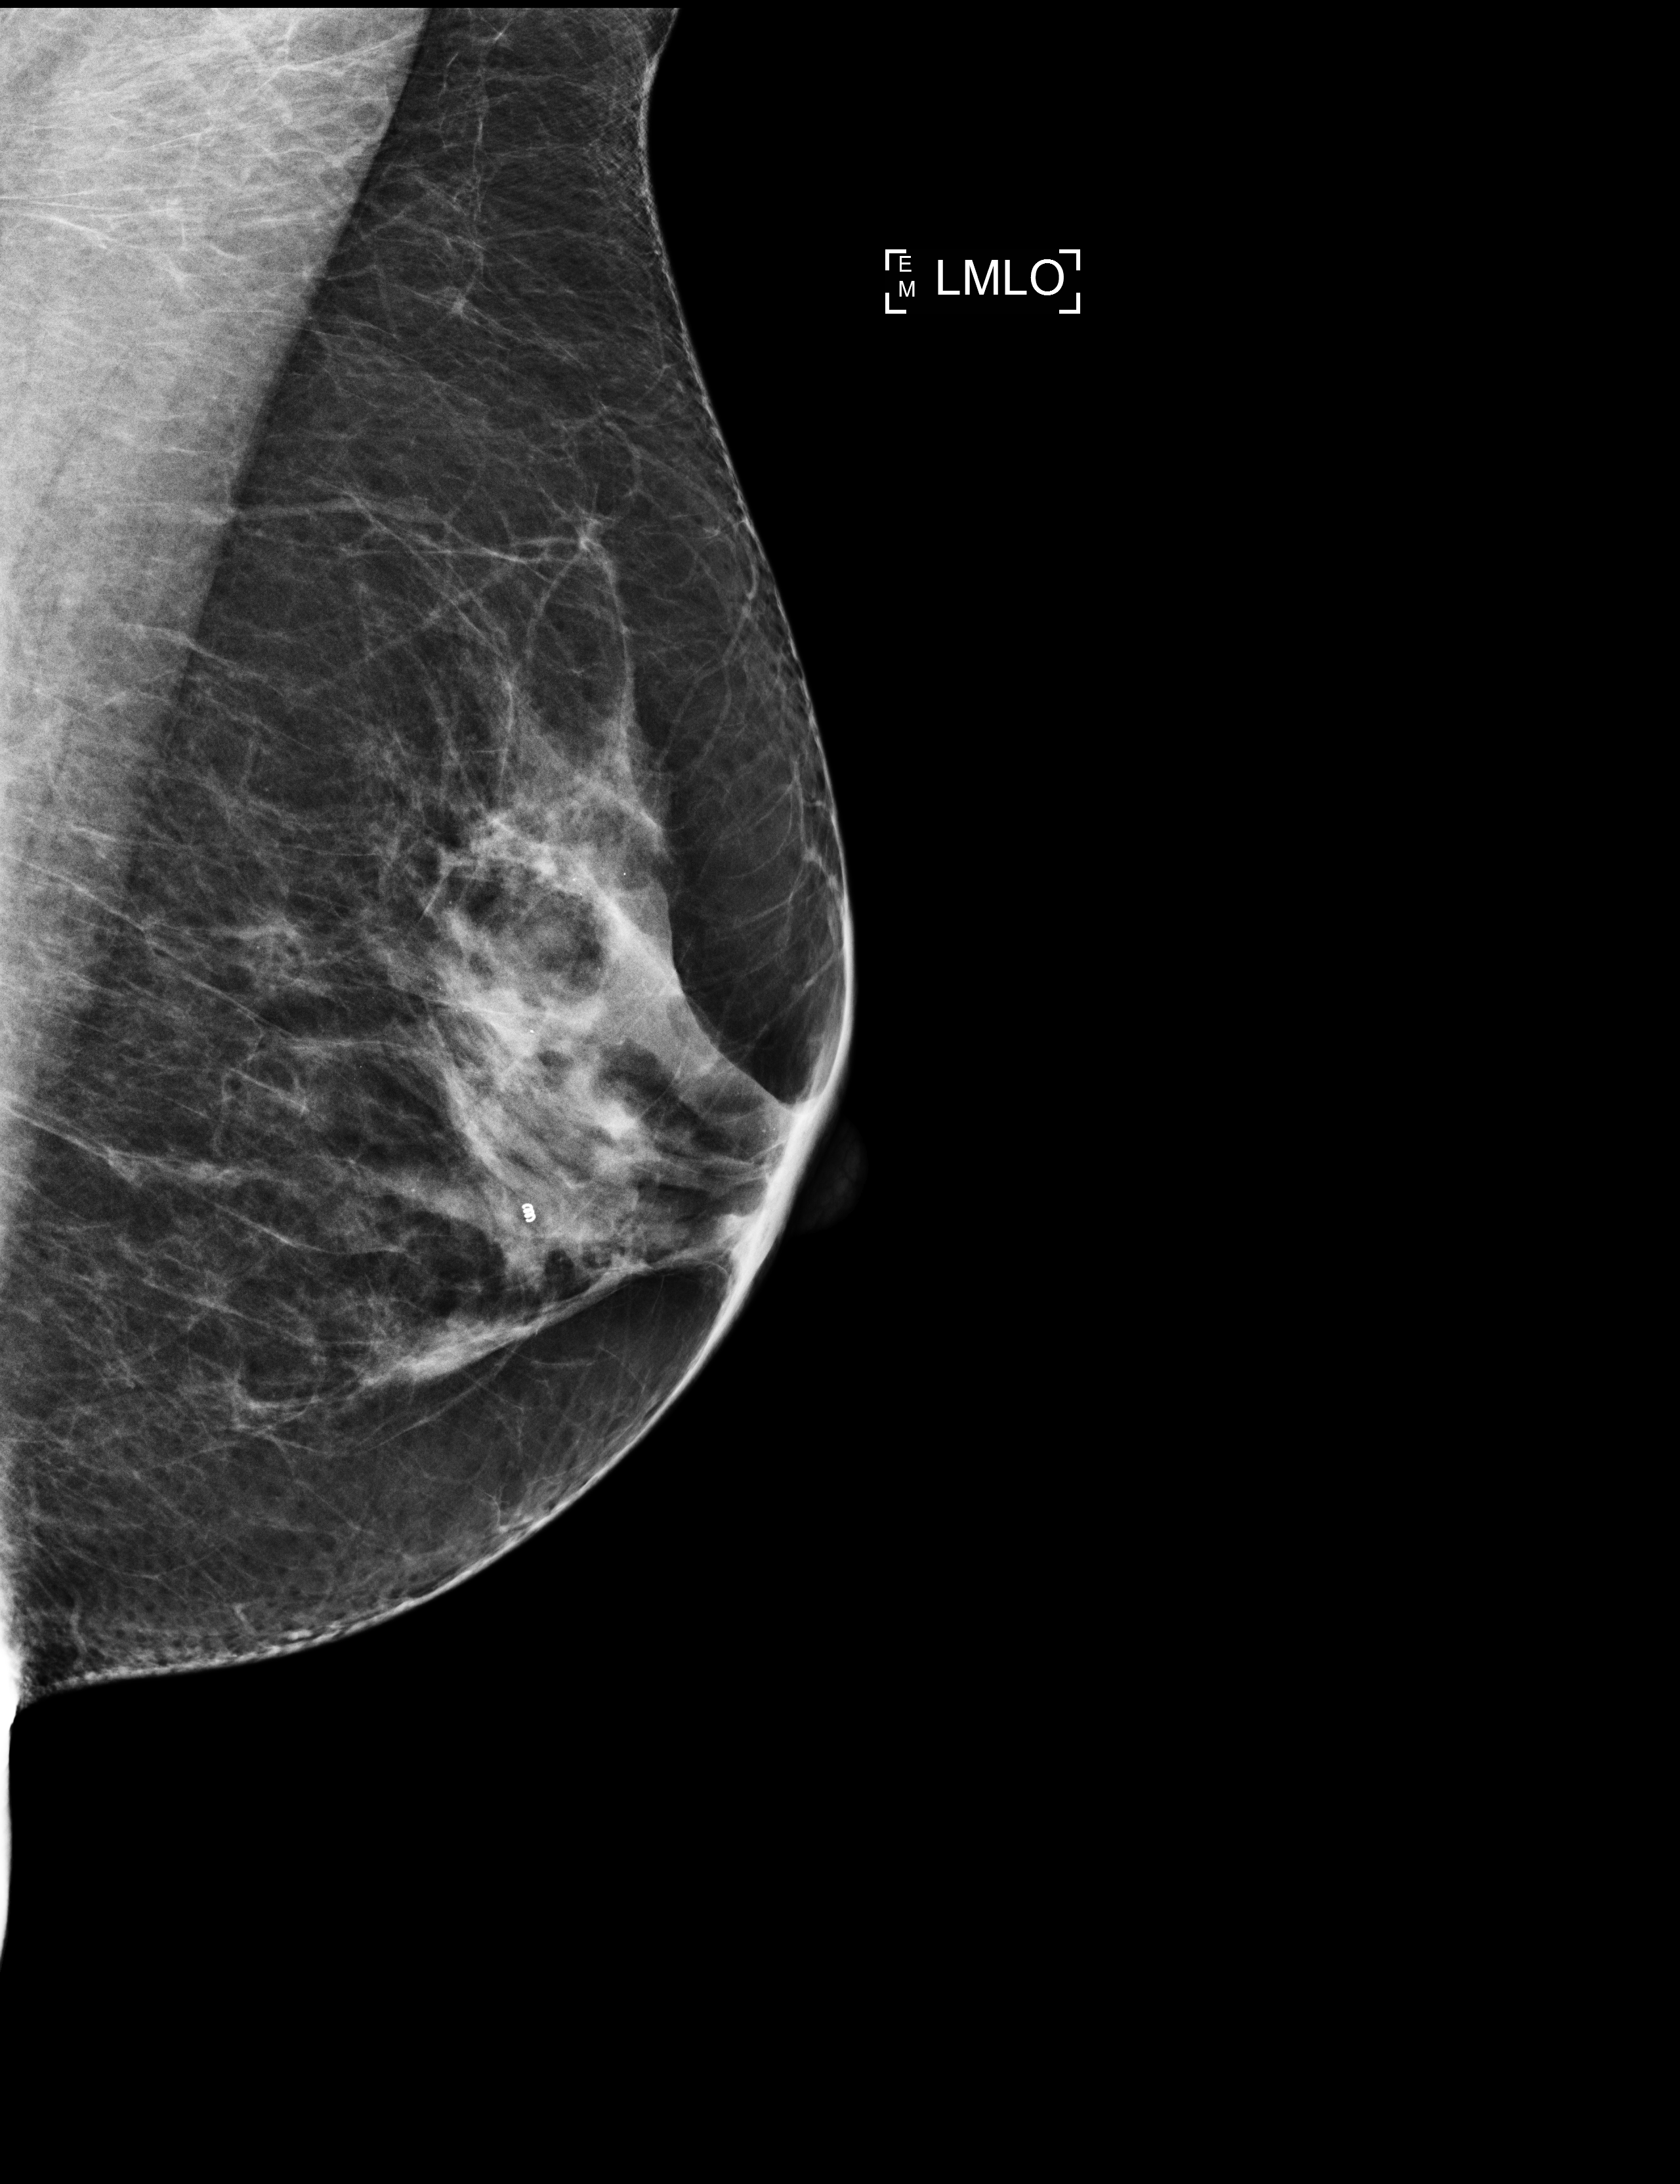
Annual screening mammography examination. Female patient, age 57 years.
Image type: full-field digital mammogram. Breast: left. Projection: MLO view.